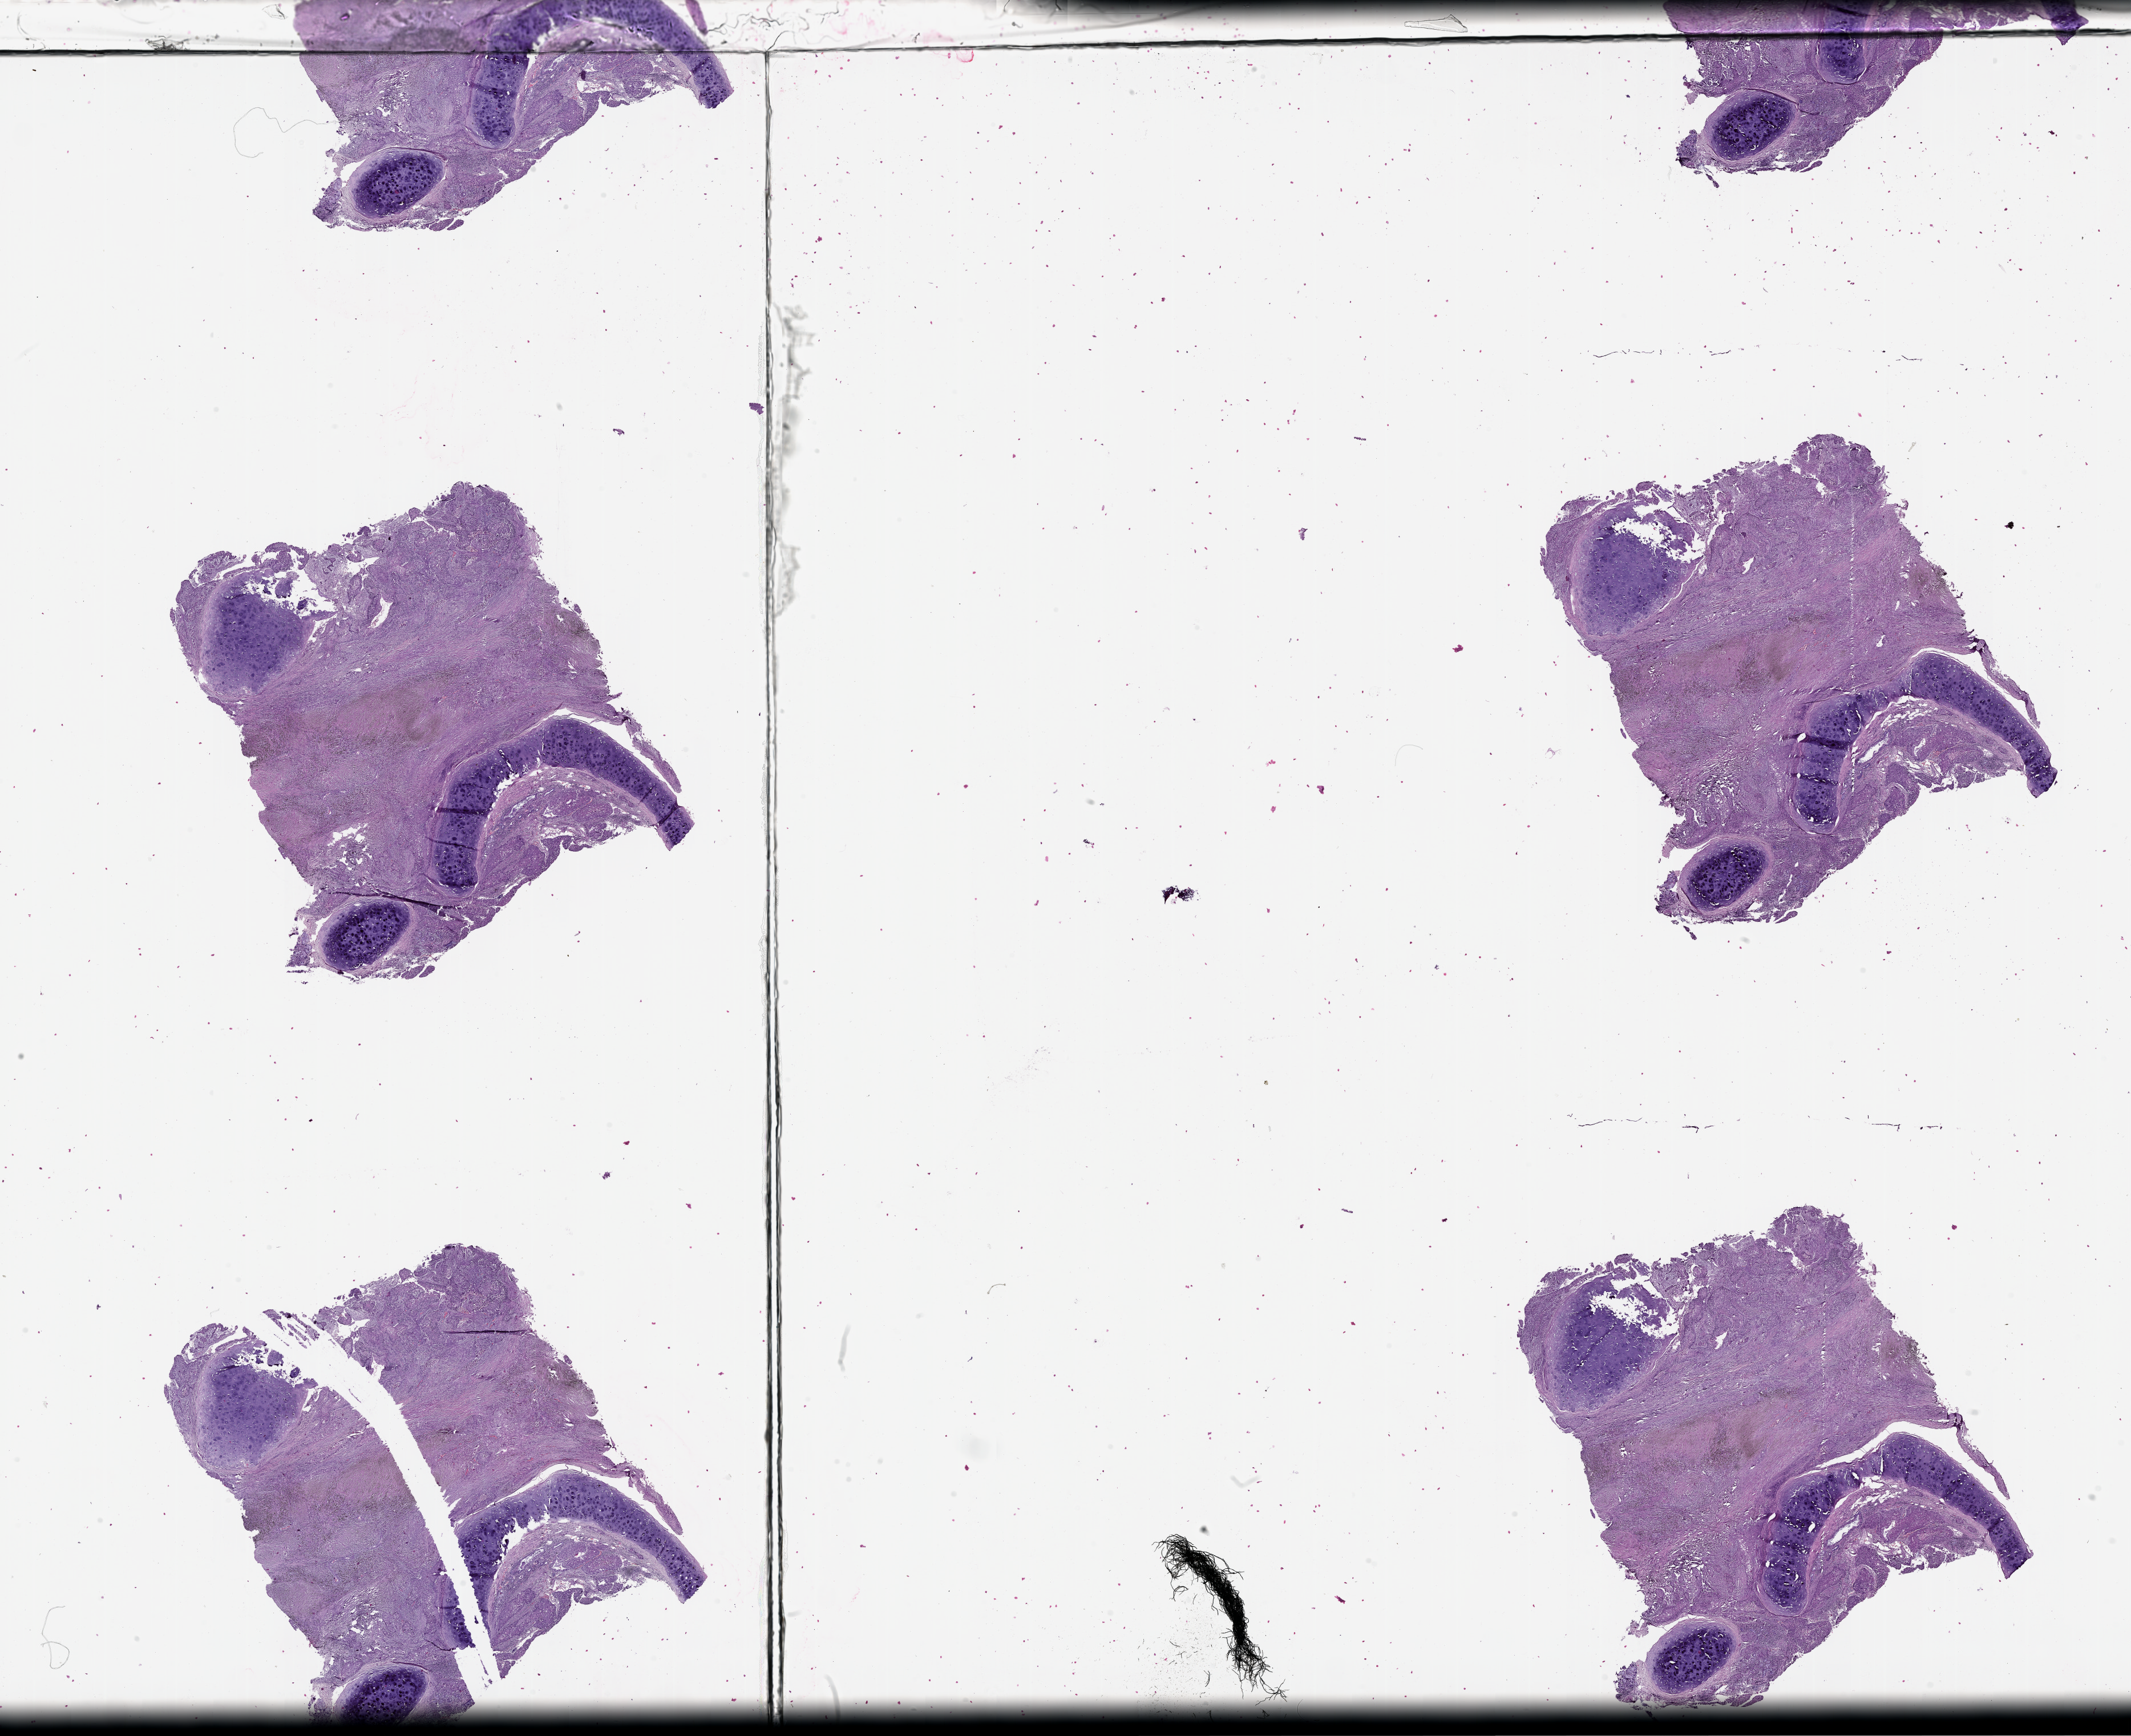
H&E whole-slide image, a low-resolution overview of the entire scanned area, about 30.1 x 24.5 mm (acquisition: 20x scan); tumour tissue sample, lung. Male, 67 y/o.
Patient diagnosis (cohort enrolment): squamous cell carcinoma (lung).